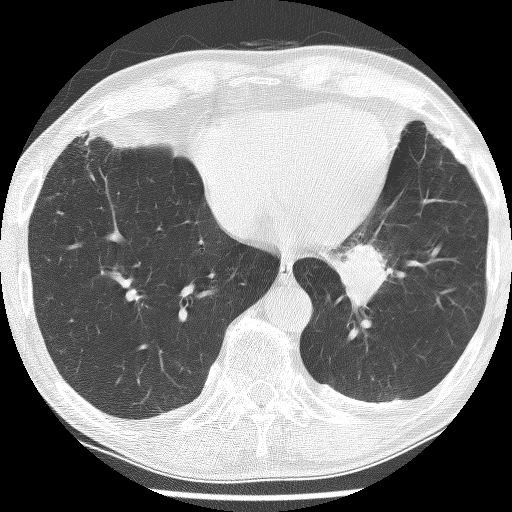
Low-dose screening chest CT, one axial slice. Position 52 of 226 along the scan axis. Reconstruction kernel BONE. Lung window (W 1500 / L -600 HU). 512 × 512 image matrix, field of view 320 × 320 mm.
Annotated regions visible in this slice (outlined manually by an expert reader):
- lesion 1 (tumor, lower lobe of left lung): bounding box <341,243,387,309> (left, top, right, bottom; pixels)